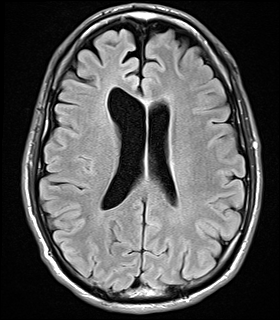
Brain MRI from a brain-tumour surgery series, one axial slice. Position 13 of 32 along the scan axis. T2 FLAIR. 280 × 320 image matrix. Case-level facts recorded for this patient, not image findings: histopathology: Glial fibroma; tumour location: Right Frontal.
Structures marked on this image (manually delineated by an expert):
- tumour: bounding box (x1, y1, x2, y2) in pixels: (117, 70, 130, 89)